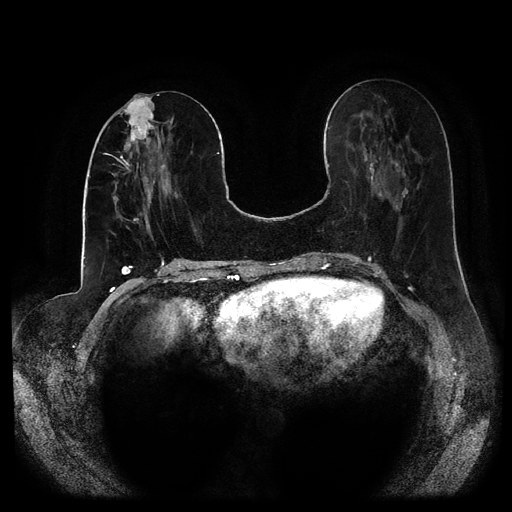
Breast MRI (dynamic contrast-enhanced, multi-phase), one axial slice. Position 39 of 116 along the scan axis. Dynamic contrast-enhanced series, time point 2 of 5 at this slice position (early post-contrast). 1.5 T. TE 2.6 ms, TR 5.2 ms. 2 mm slice thickness. 512 × 512 image matrix. Patient: female, 53 years.
Structures marked on this image (semi-automatically segmented with operator editing):
- breast lesion (labelled 'tumour' in the annotation; benign lesions carry a separate 'benign' label): box from (x=118, y=96) to (x=157, y=153) px